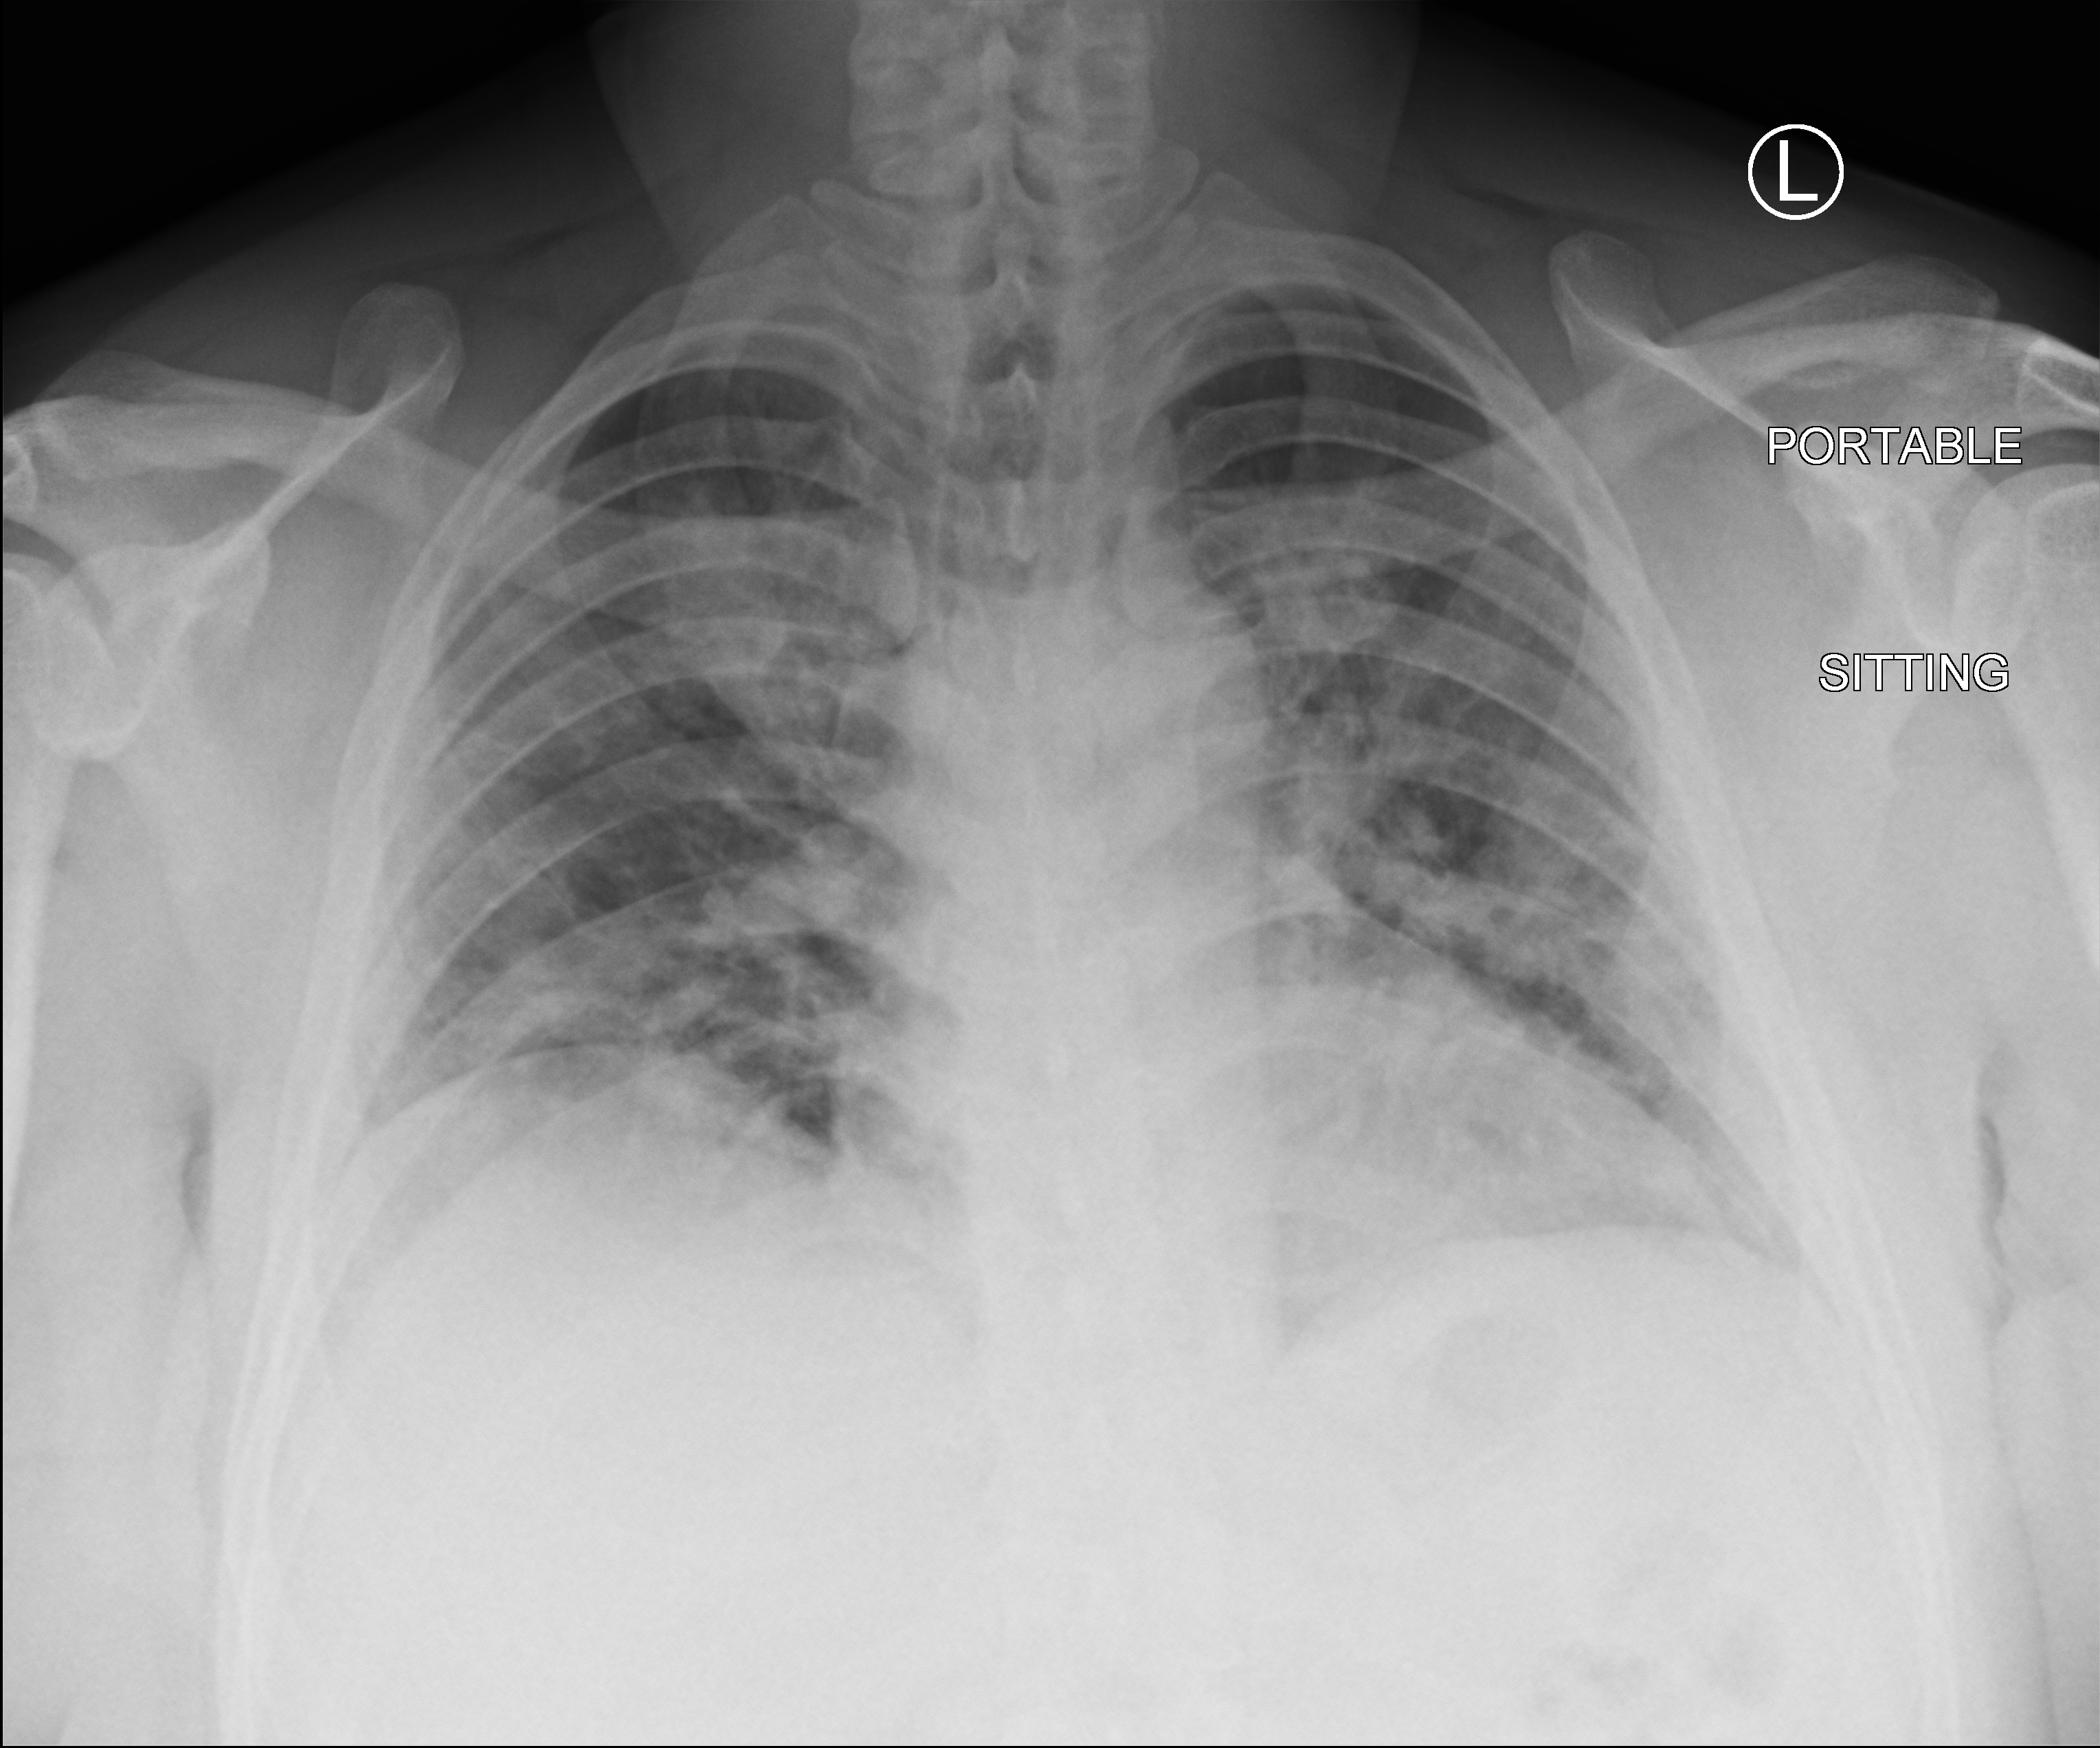
Bedside chest radiograph (computed radiography), anteroposterior (AP) projection. Patient hospitalised with COVID-19; male, aged 18–59 years.
From the hospital-stay record, not from the radiograph (when in the stay this image was taken is not recorded):
- mechanically ventilated during this hospital stay: yes
- admitted to intensive care during this hospital stay: yes